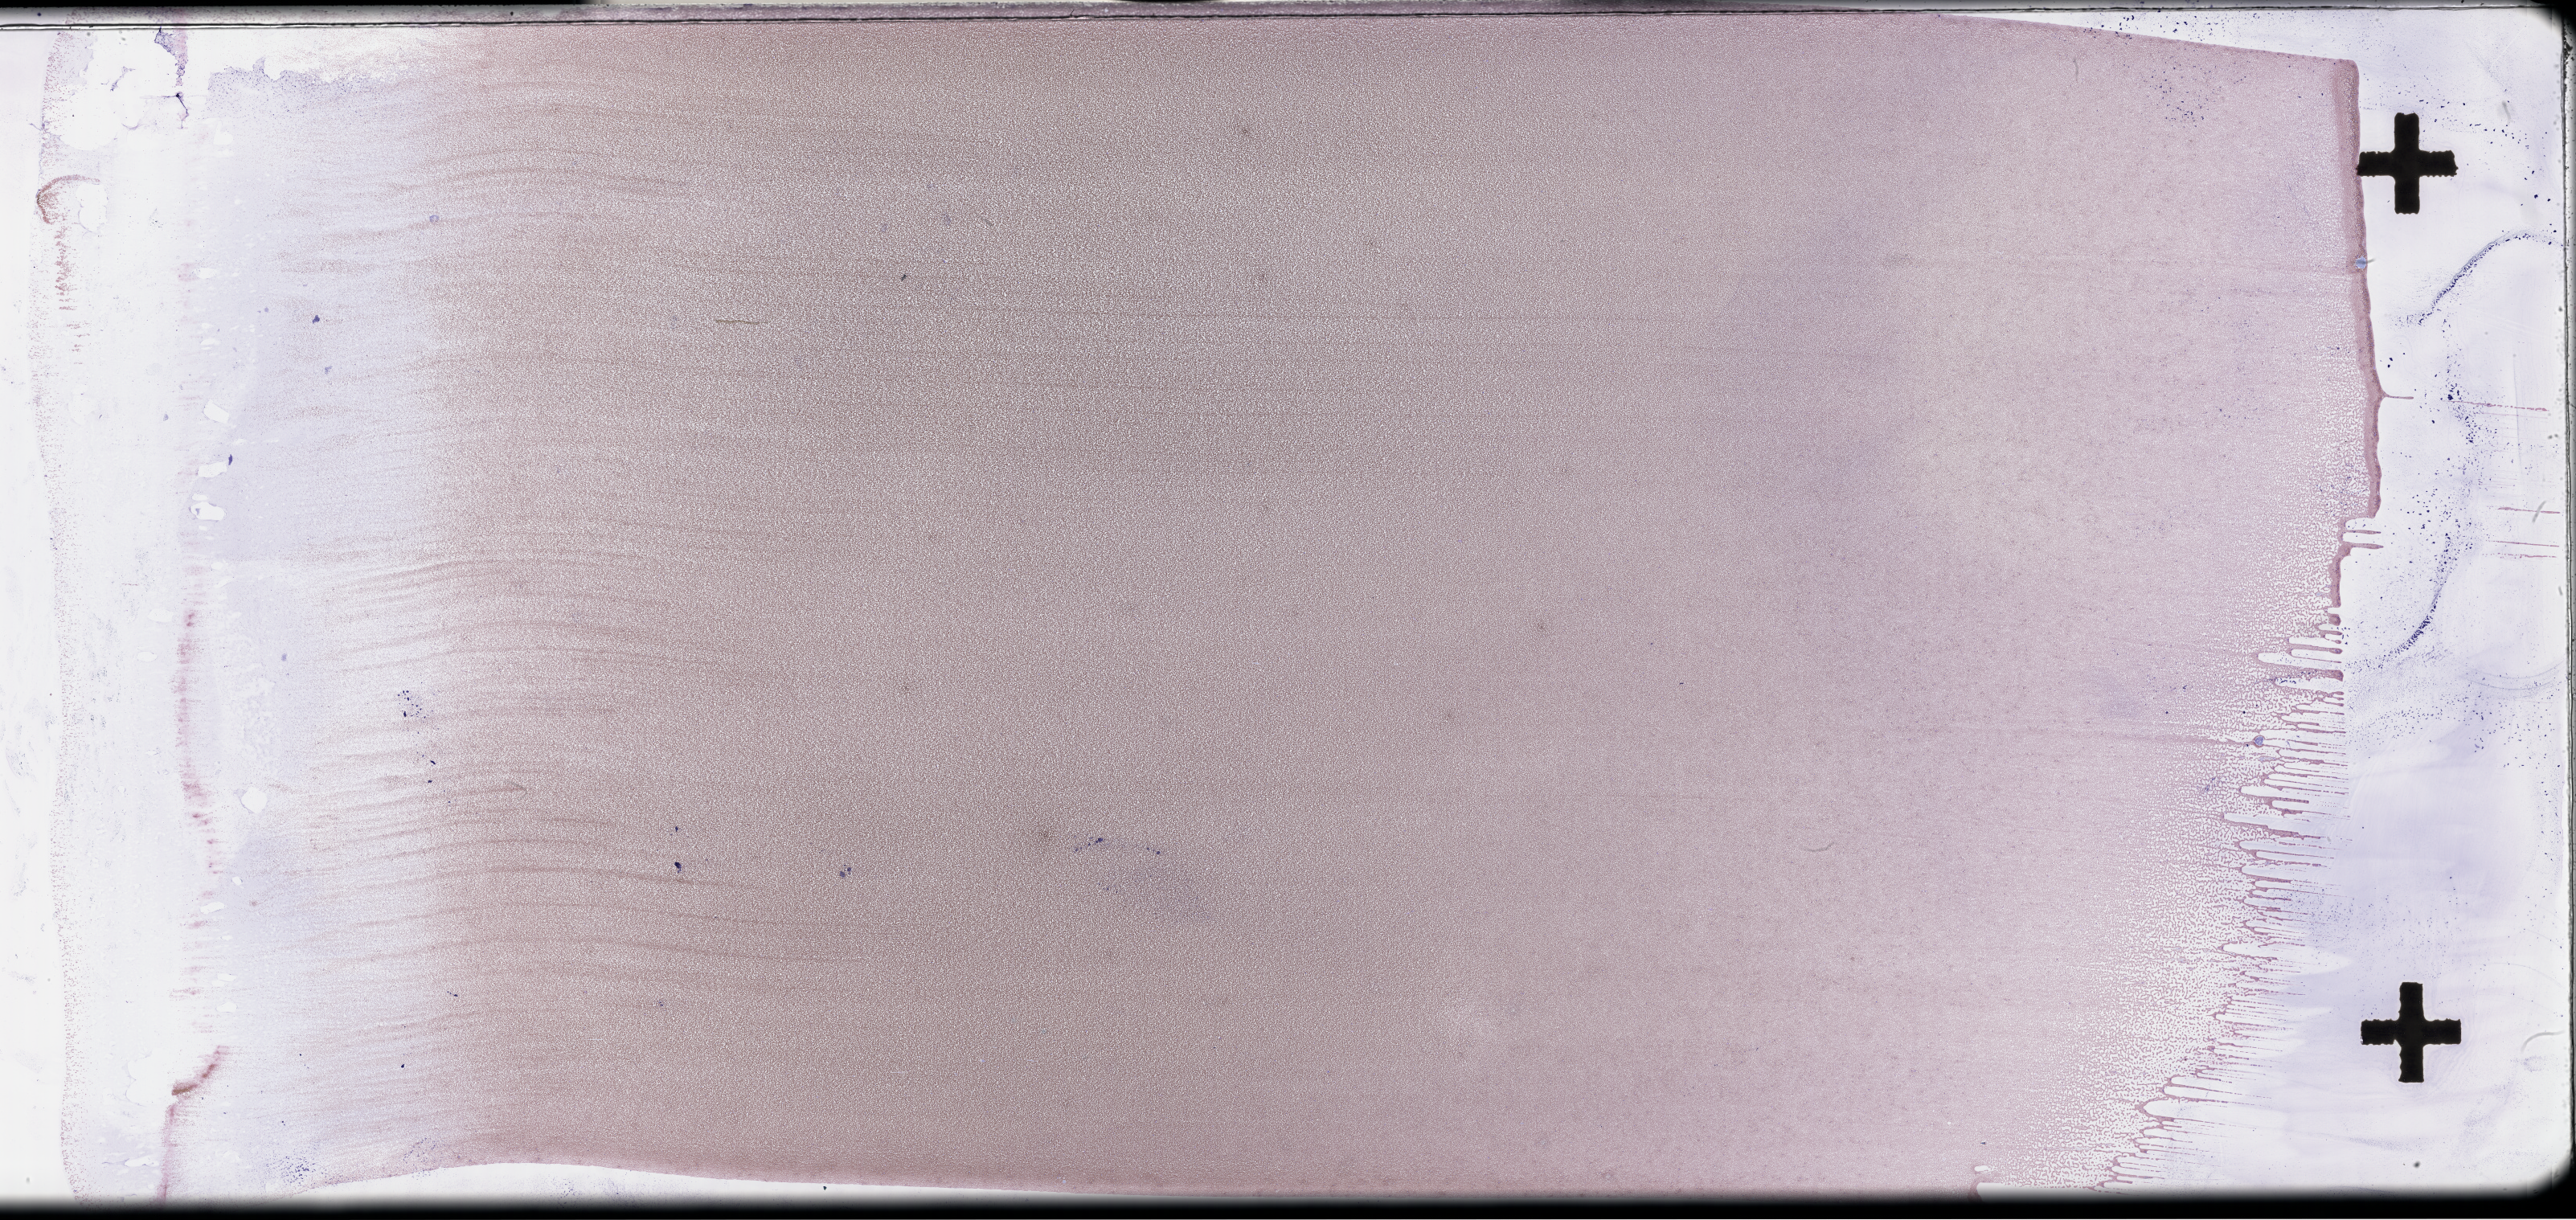
Wright-Giemsa-stained whole blood smear, whole-slide image — whole scanned area (about 51.8 x 24.5 mm) shown as a low-resolution overview, collected on treatment. Patient sex: female.
- from a patient with: Acute Myeloid Leukemia Not Otherwise Specified